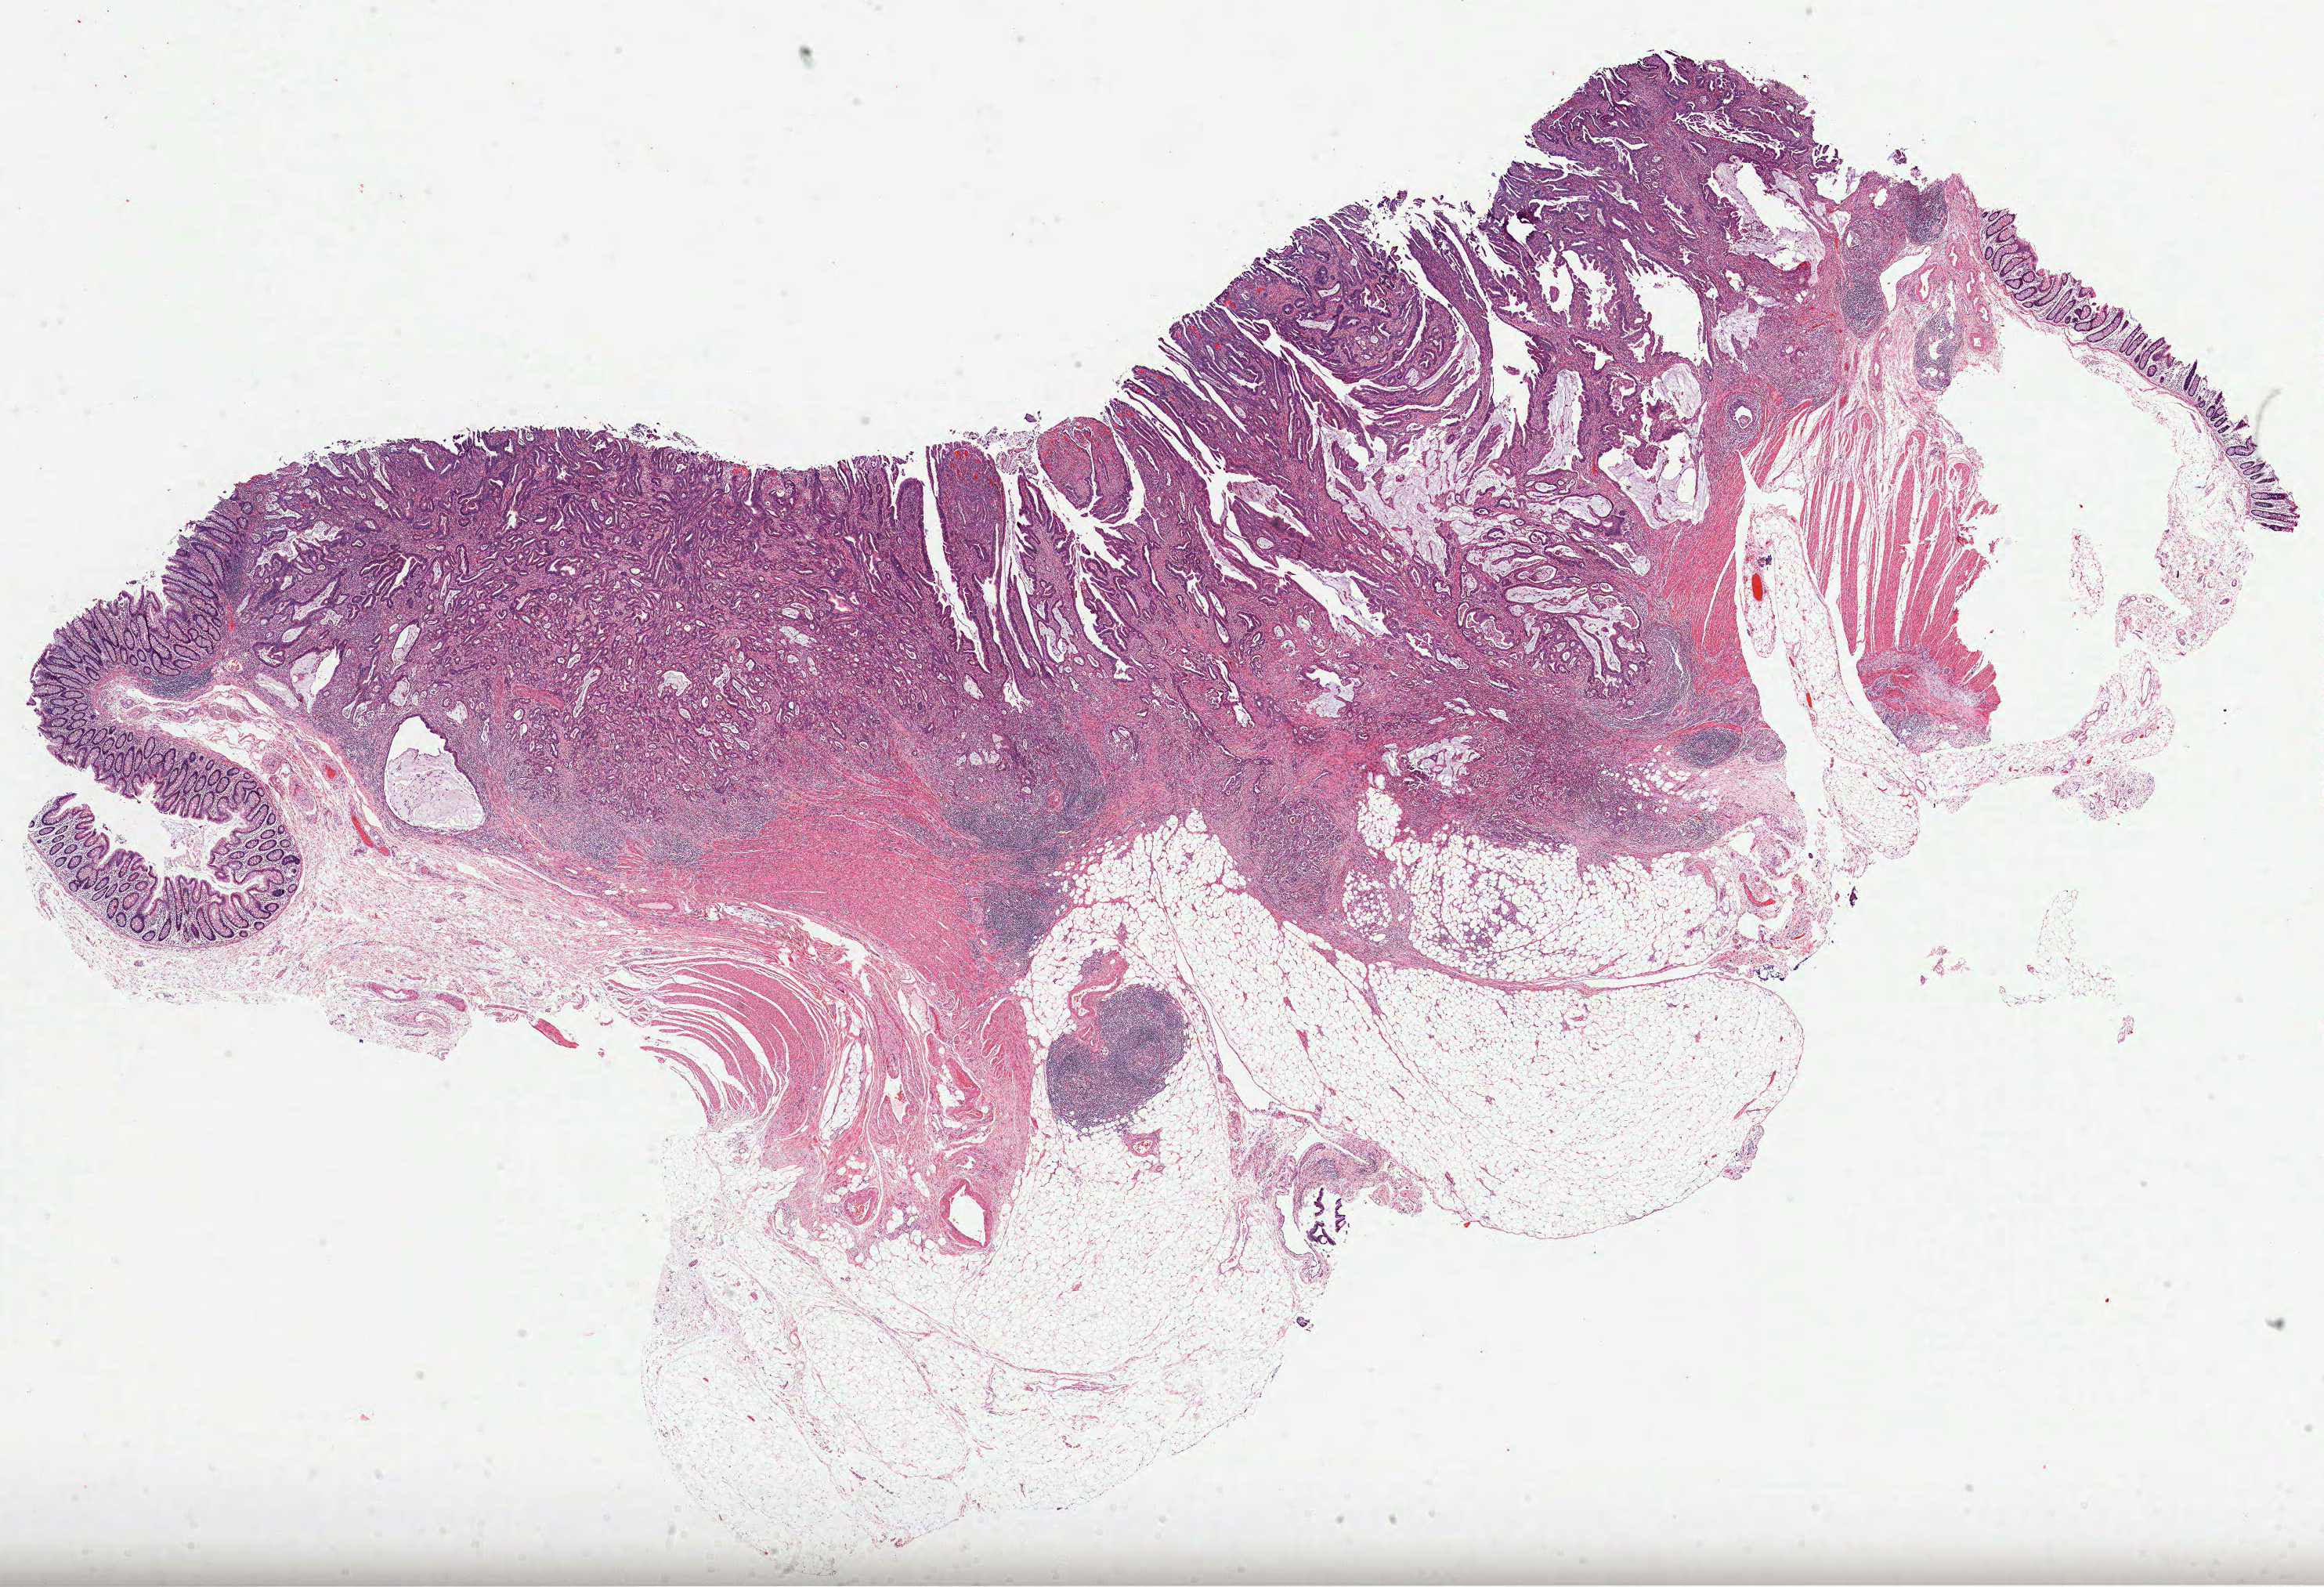
Whole-slide histology image, H&E-stained — a low-resolution overview of the entire scanned area, about 23.9 x 16.3 mm. FFPE section. Sample: primary tumour, colon. Female patient; age at initial diagnosis 79 years.
- histologic diagnosis: Mucinous adenocarcinoma
- AJCC pathologic stage: IIA (6th edition)
- TNM: T3 N0 M0
- lymph nodes positive (case pathology): 0 of 30 examined